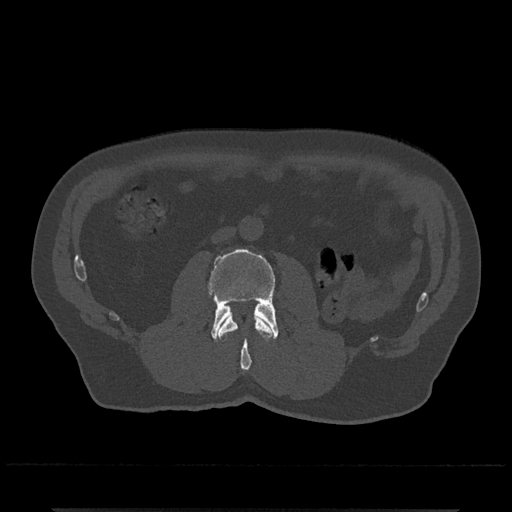
CT including the spine, one axial slice; position 247 of 797 along the scan axis; bone window (W 1800 / L 400 HU); 0.5 mm slice thickness; 512 × 512 image matrix. Male patient, age 67 years. Case-level facts recorded for this patient, not image findings: primary cancer: prostate.
Outlined on this slice (semi-automatically segmented with operator editing):
- L2 vertebra: box from (x=218, y=315) to (x=272, y=372) px
- L3 vertebra: (x=208, y=248)–(x=279, y=341)